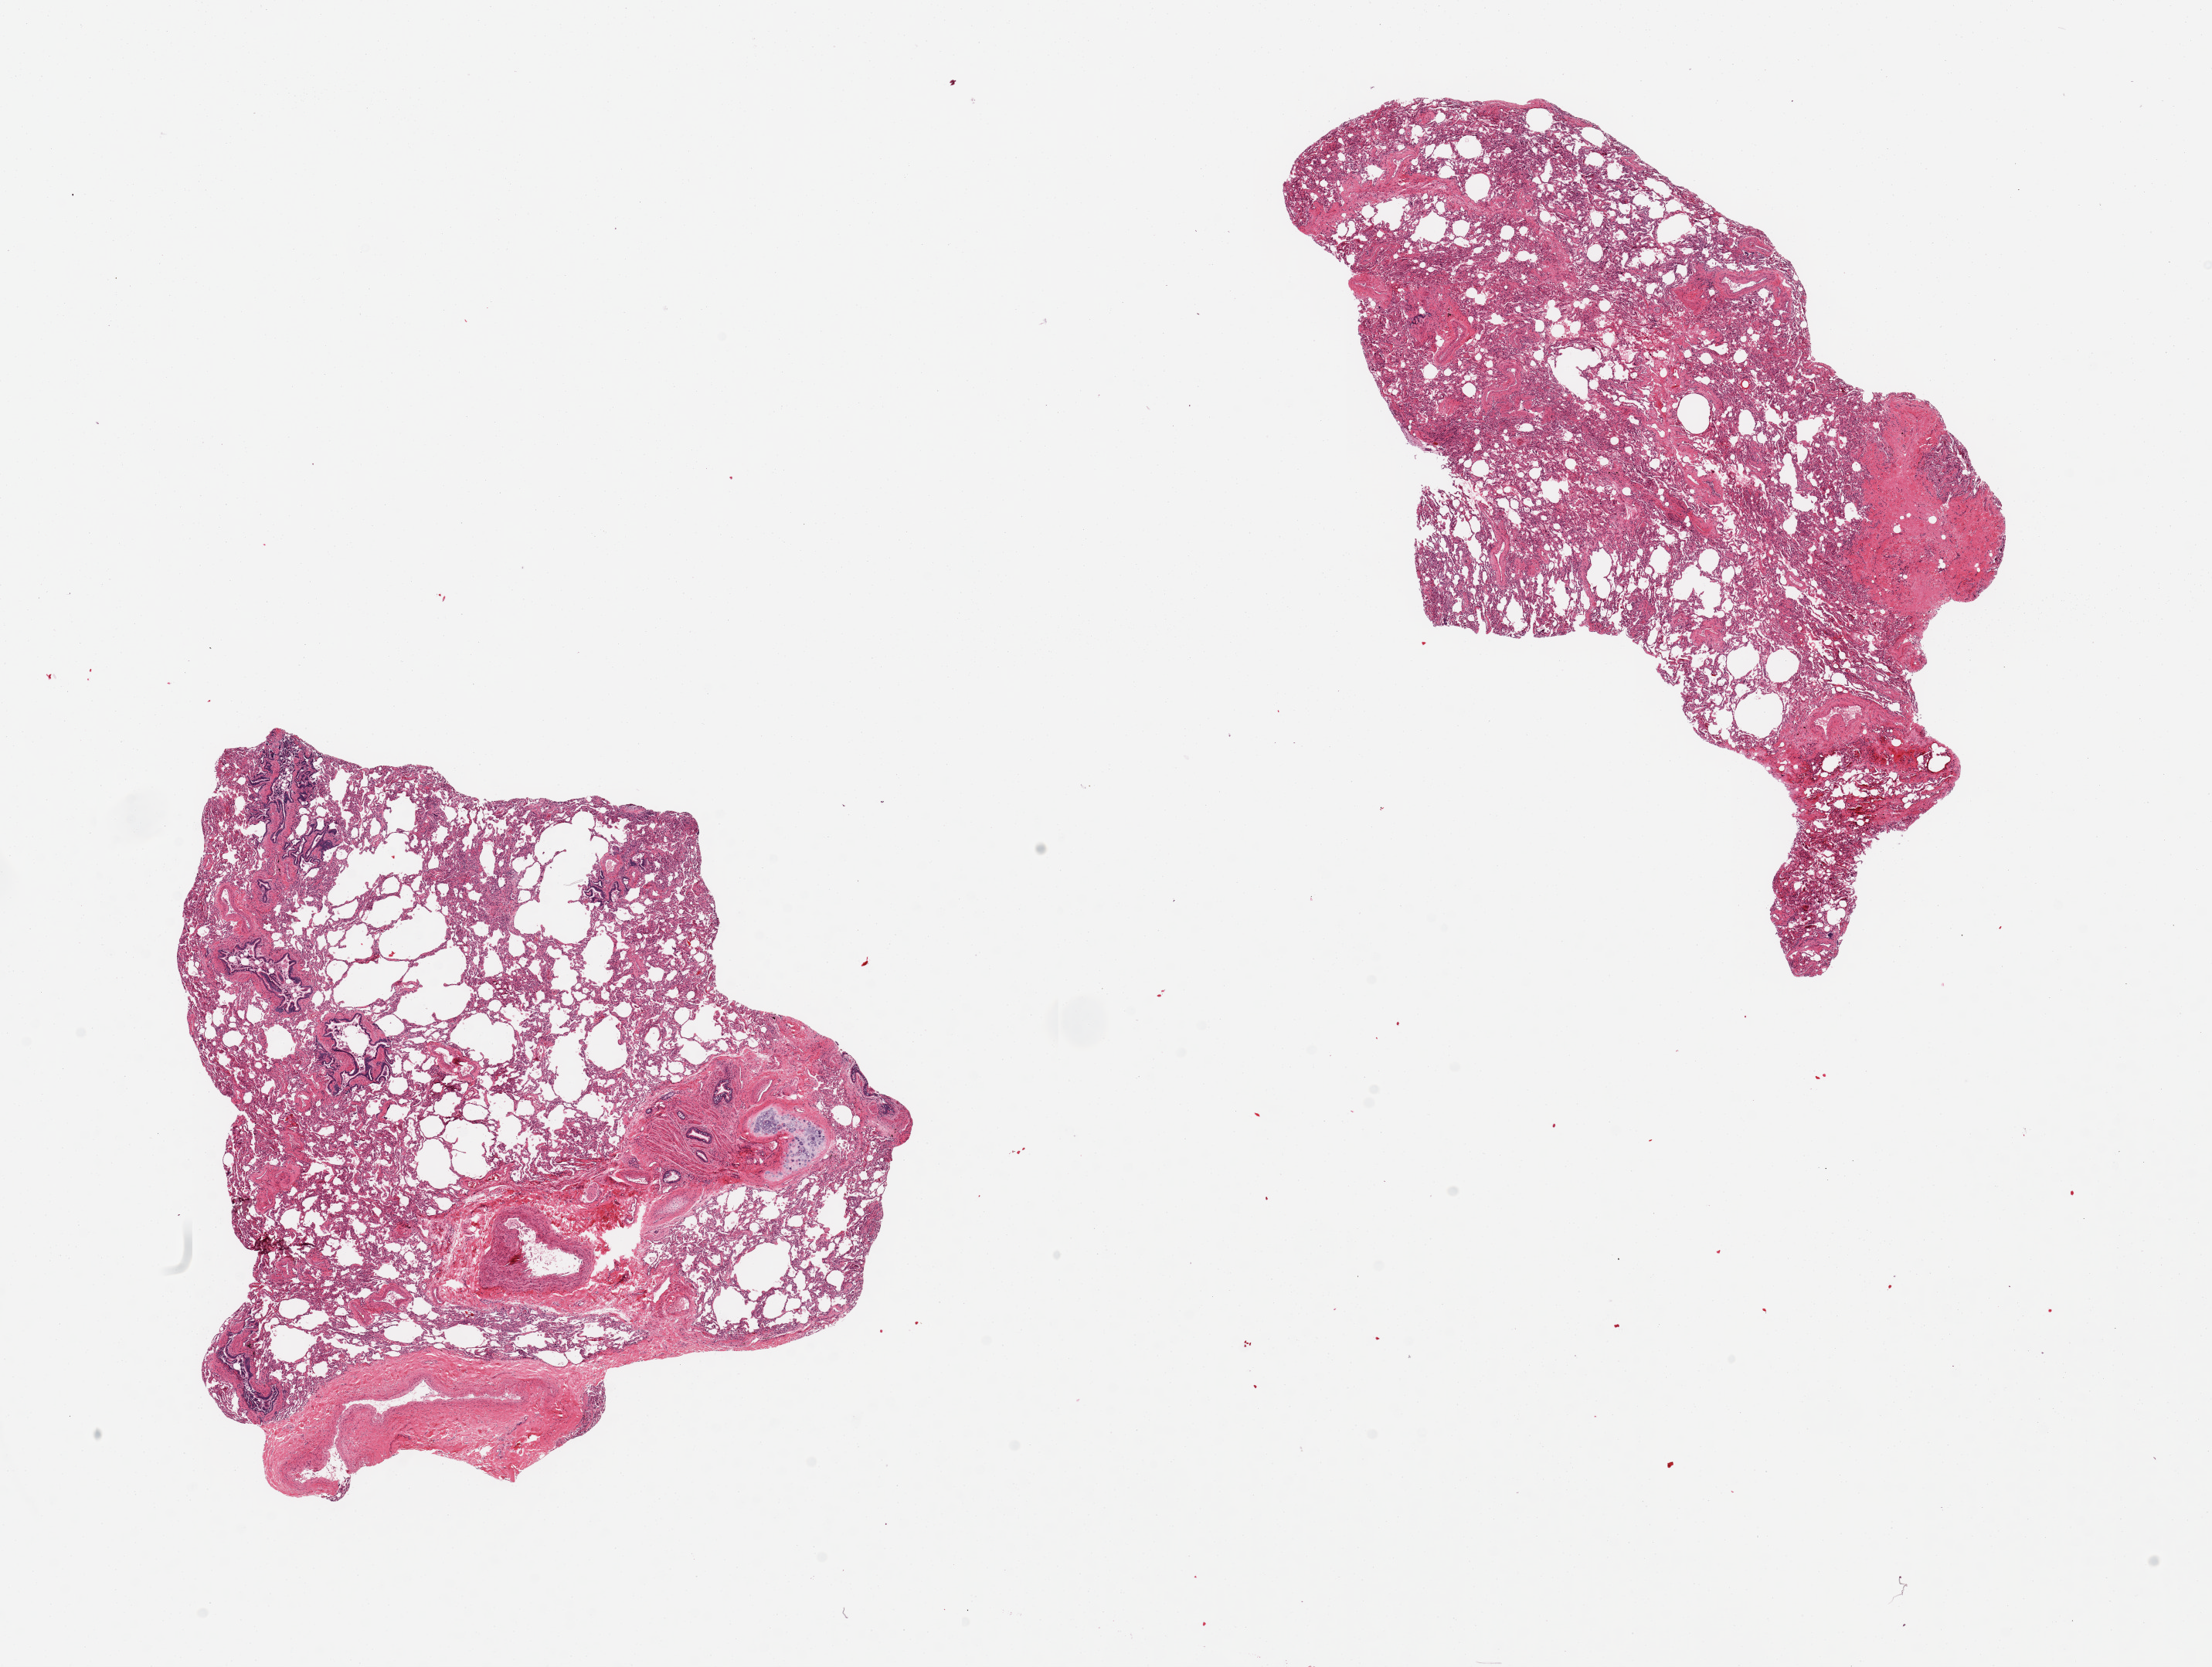
H&E whole-slide image, brightfield — whole scanned area (about 22.6 x 17.1 mm, slide scanned at 20x) shown as a low-resolution overview. PAXgene-fixed, paraffin-embedded tissue. Target tissue: lung. Tissue donor sample. Donor sex: female.
Review note (as recorded): 2 pieces, some emphysematous change and fibrosis, bronchus and adjacent cartilage.